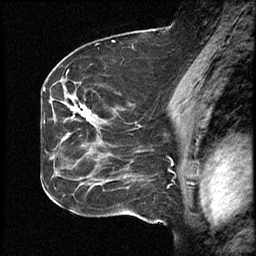
Breast MRI (dynamic contrast-enhanced), one sagittal slice; position 26 of 46 along the scan axis; dynamic contrast-enhanced study with each time point stored as its own series, time point 2 of 4 at this slice position (early post-contrast, ordered by acquisition time); 1.5 T; TE 4.2 ms, TR 18.3 ms; 256 × 256 image matrix, field of view 200 × 200 mm. Case-level facts recorded for this patient, not image findings: setting: breast cancer imaged before/during neoadjuvant chemotherapy; receptor status: HR-positive, HER2-negative.
Structures marked on this image (semi-automatic segmentation, software-assisted and operator-edited):
- analysis volume of interest (the breast-tissue region the enhancement analysis was run in; not a lesion): bounding box <64,72,111,203> (left, top, right, bottom; pixels)
- tumour enhancement mask (voxels above the 100 % enhancement threshold inside the analysis volume of interest): <79,109,91,115>